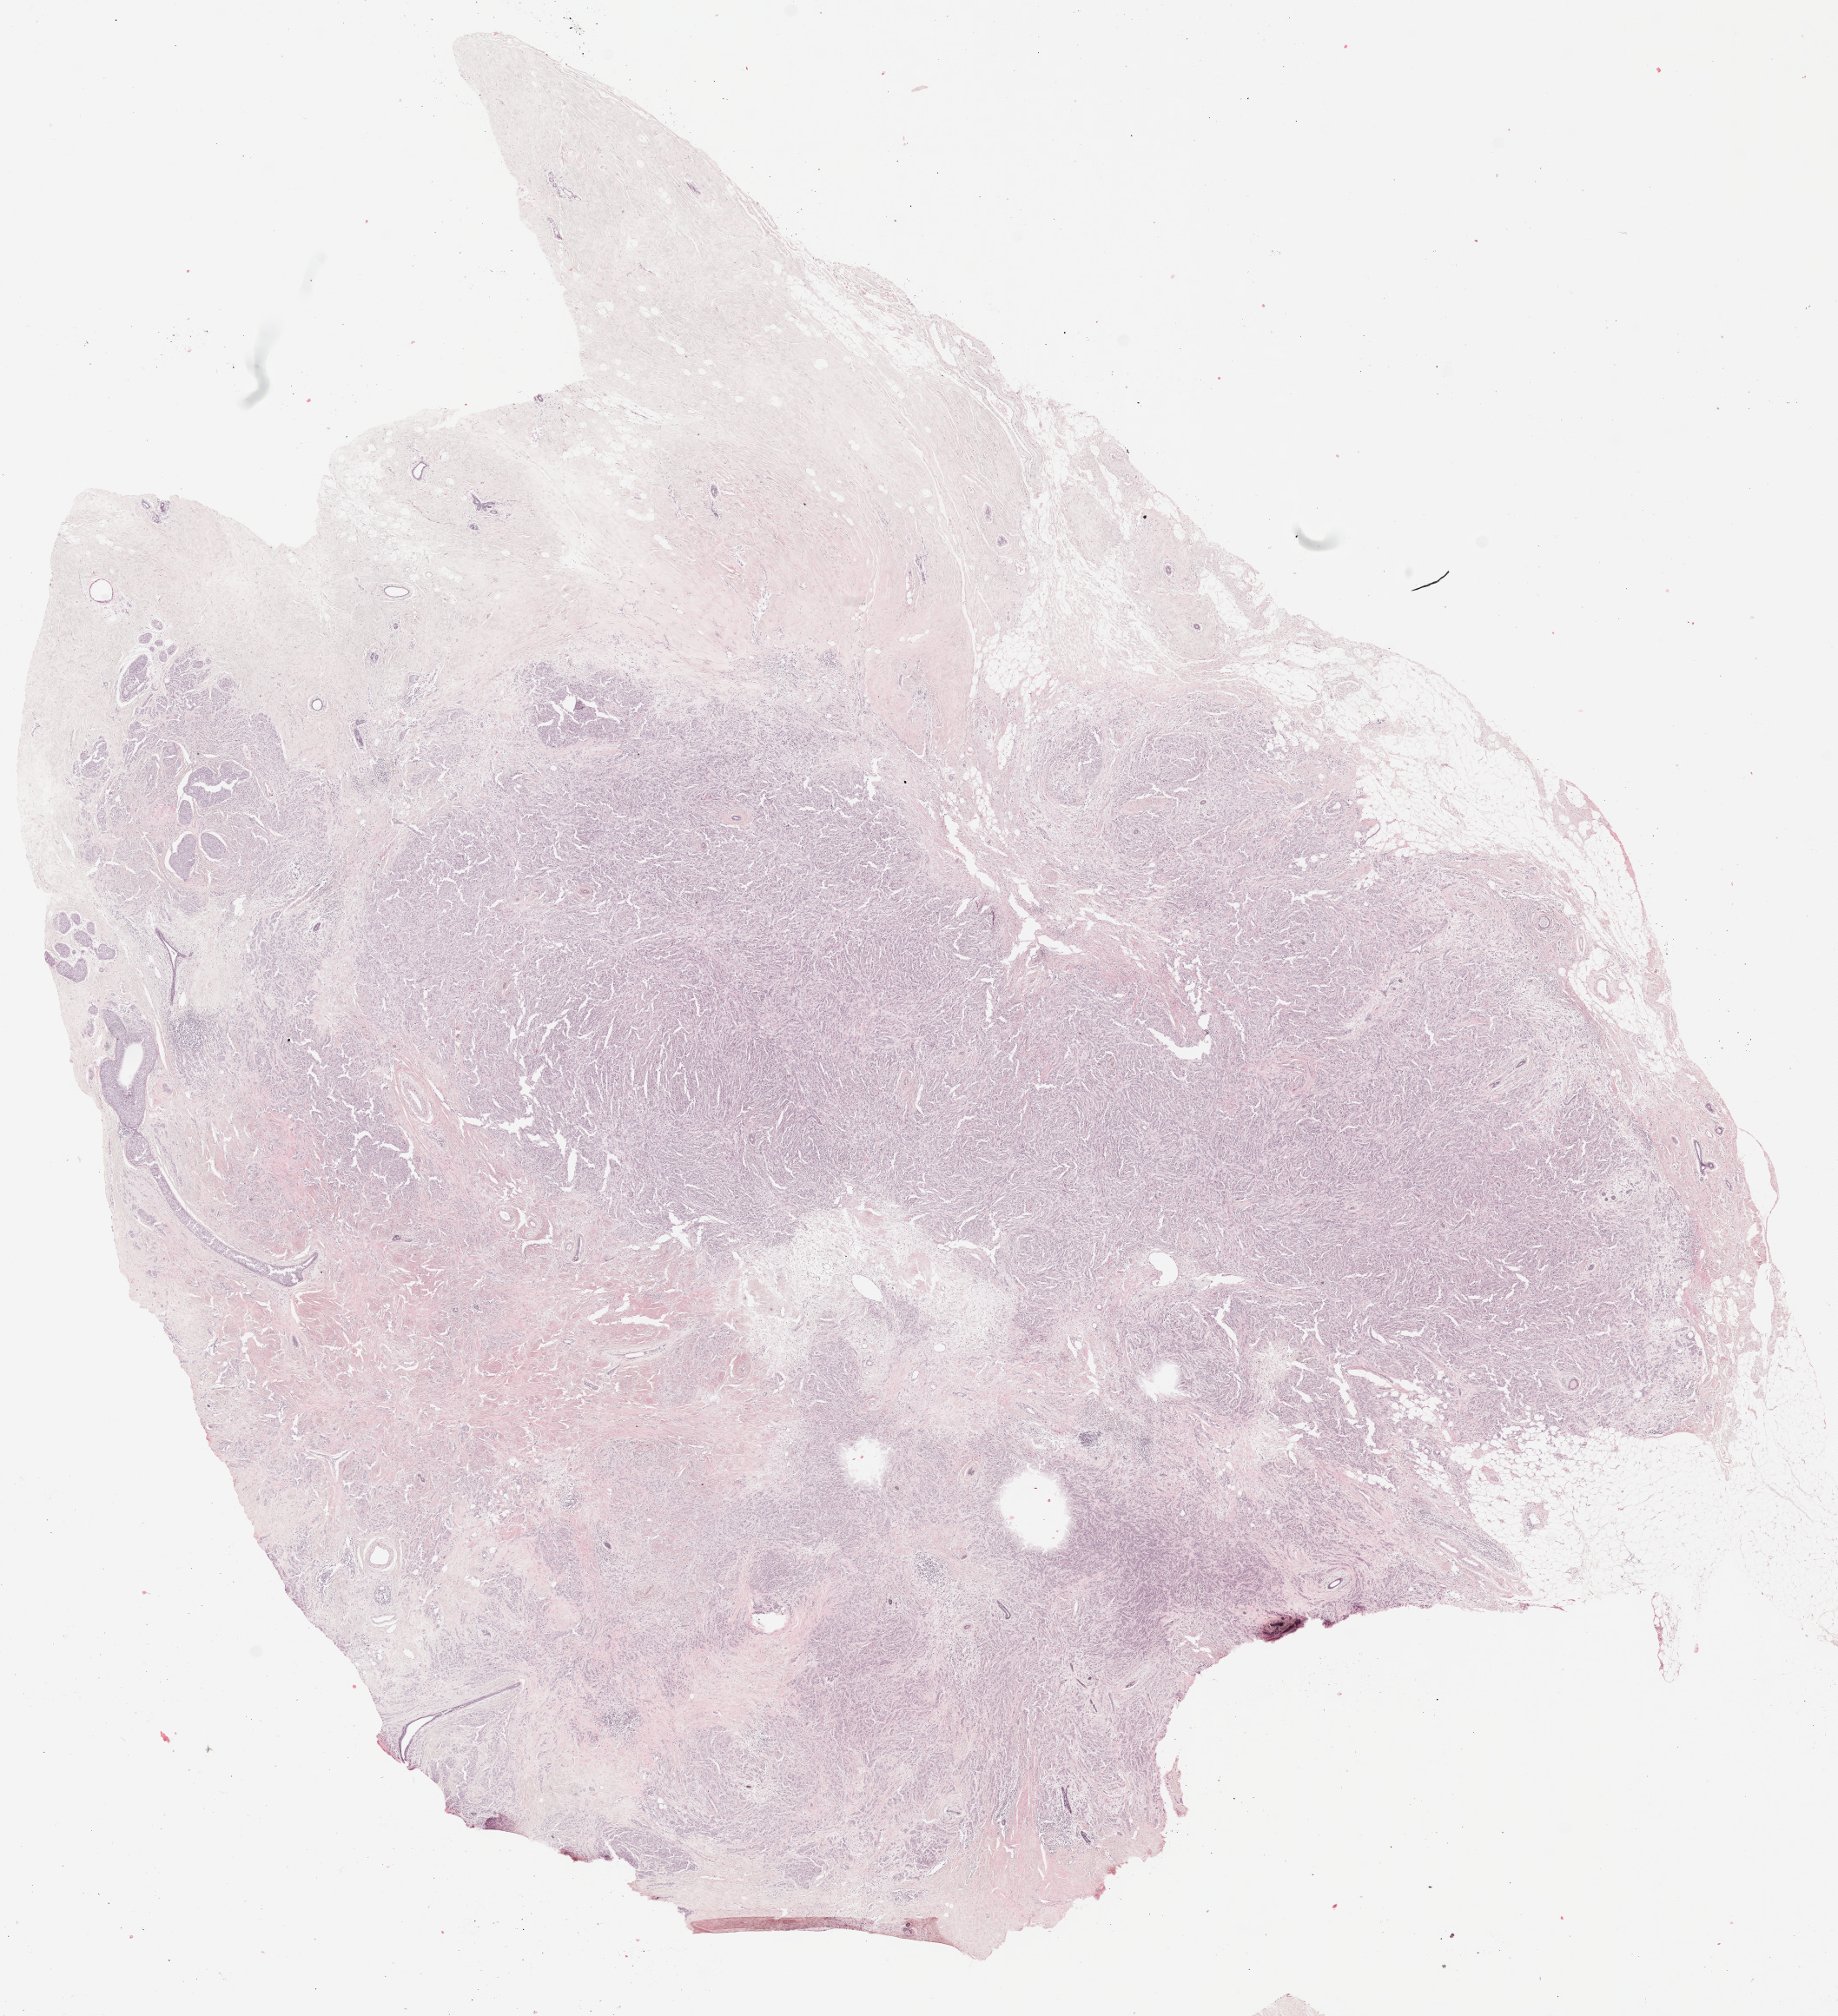
Whole-slide histology image, Hematoxylin and eosin (H&E) stained, whole scanned area (about 16.9 x 18.5 mm, from a 20x scan) shown as a low-resolution overview, formalin-fixed paraffin-embedded (FFPE) diagnostic section, breast, primary tumour sample. Patient: female, age at initial diagnosis 75 years.
• lymph nodes positive (case pathology): 0 of 4 examined
• laterality: right
• TNM: T2 N0 (i+) M0
• AJCC pathologic stage: IIA (6th edition)
• pathologic diagnosis: Pleomorphic carcinoma